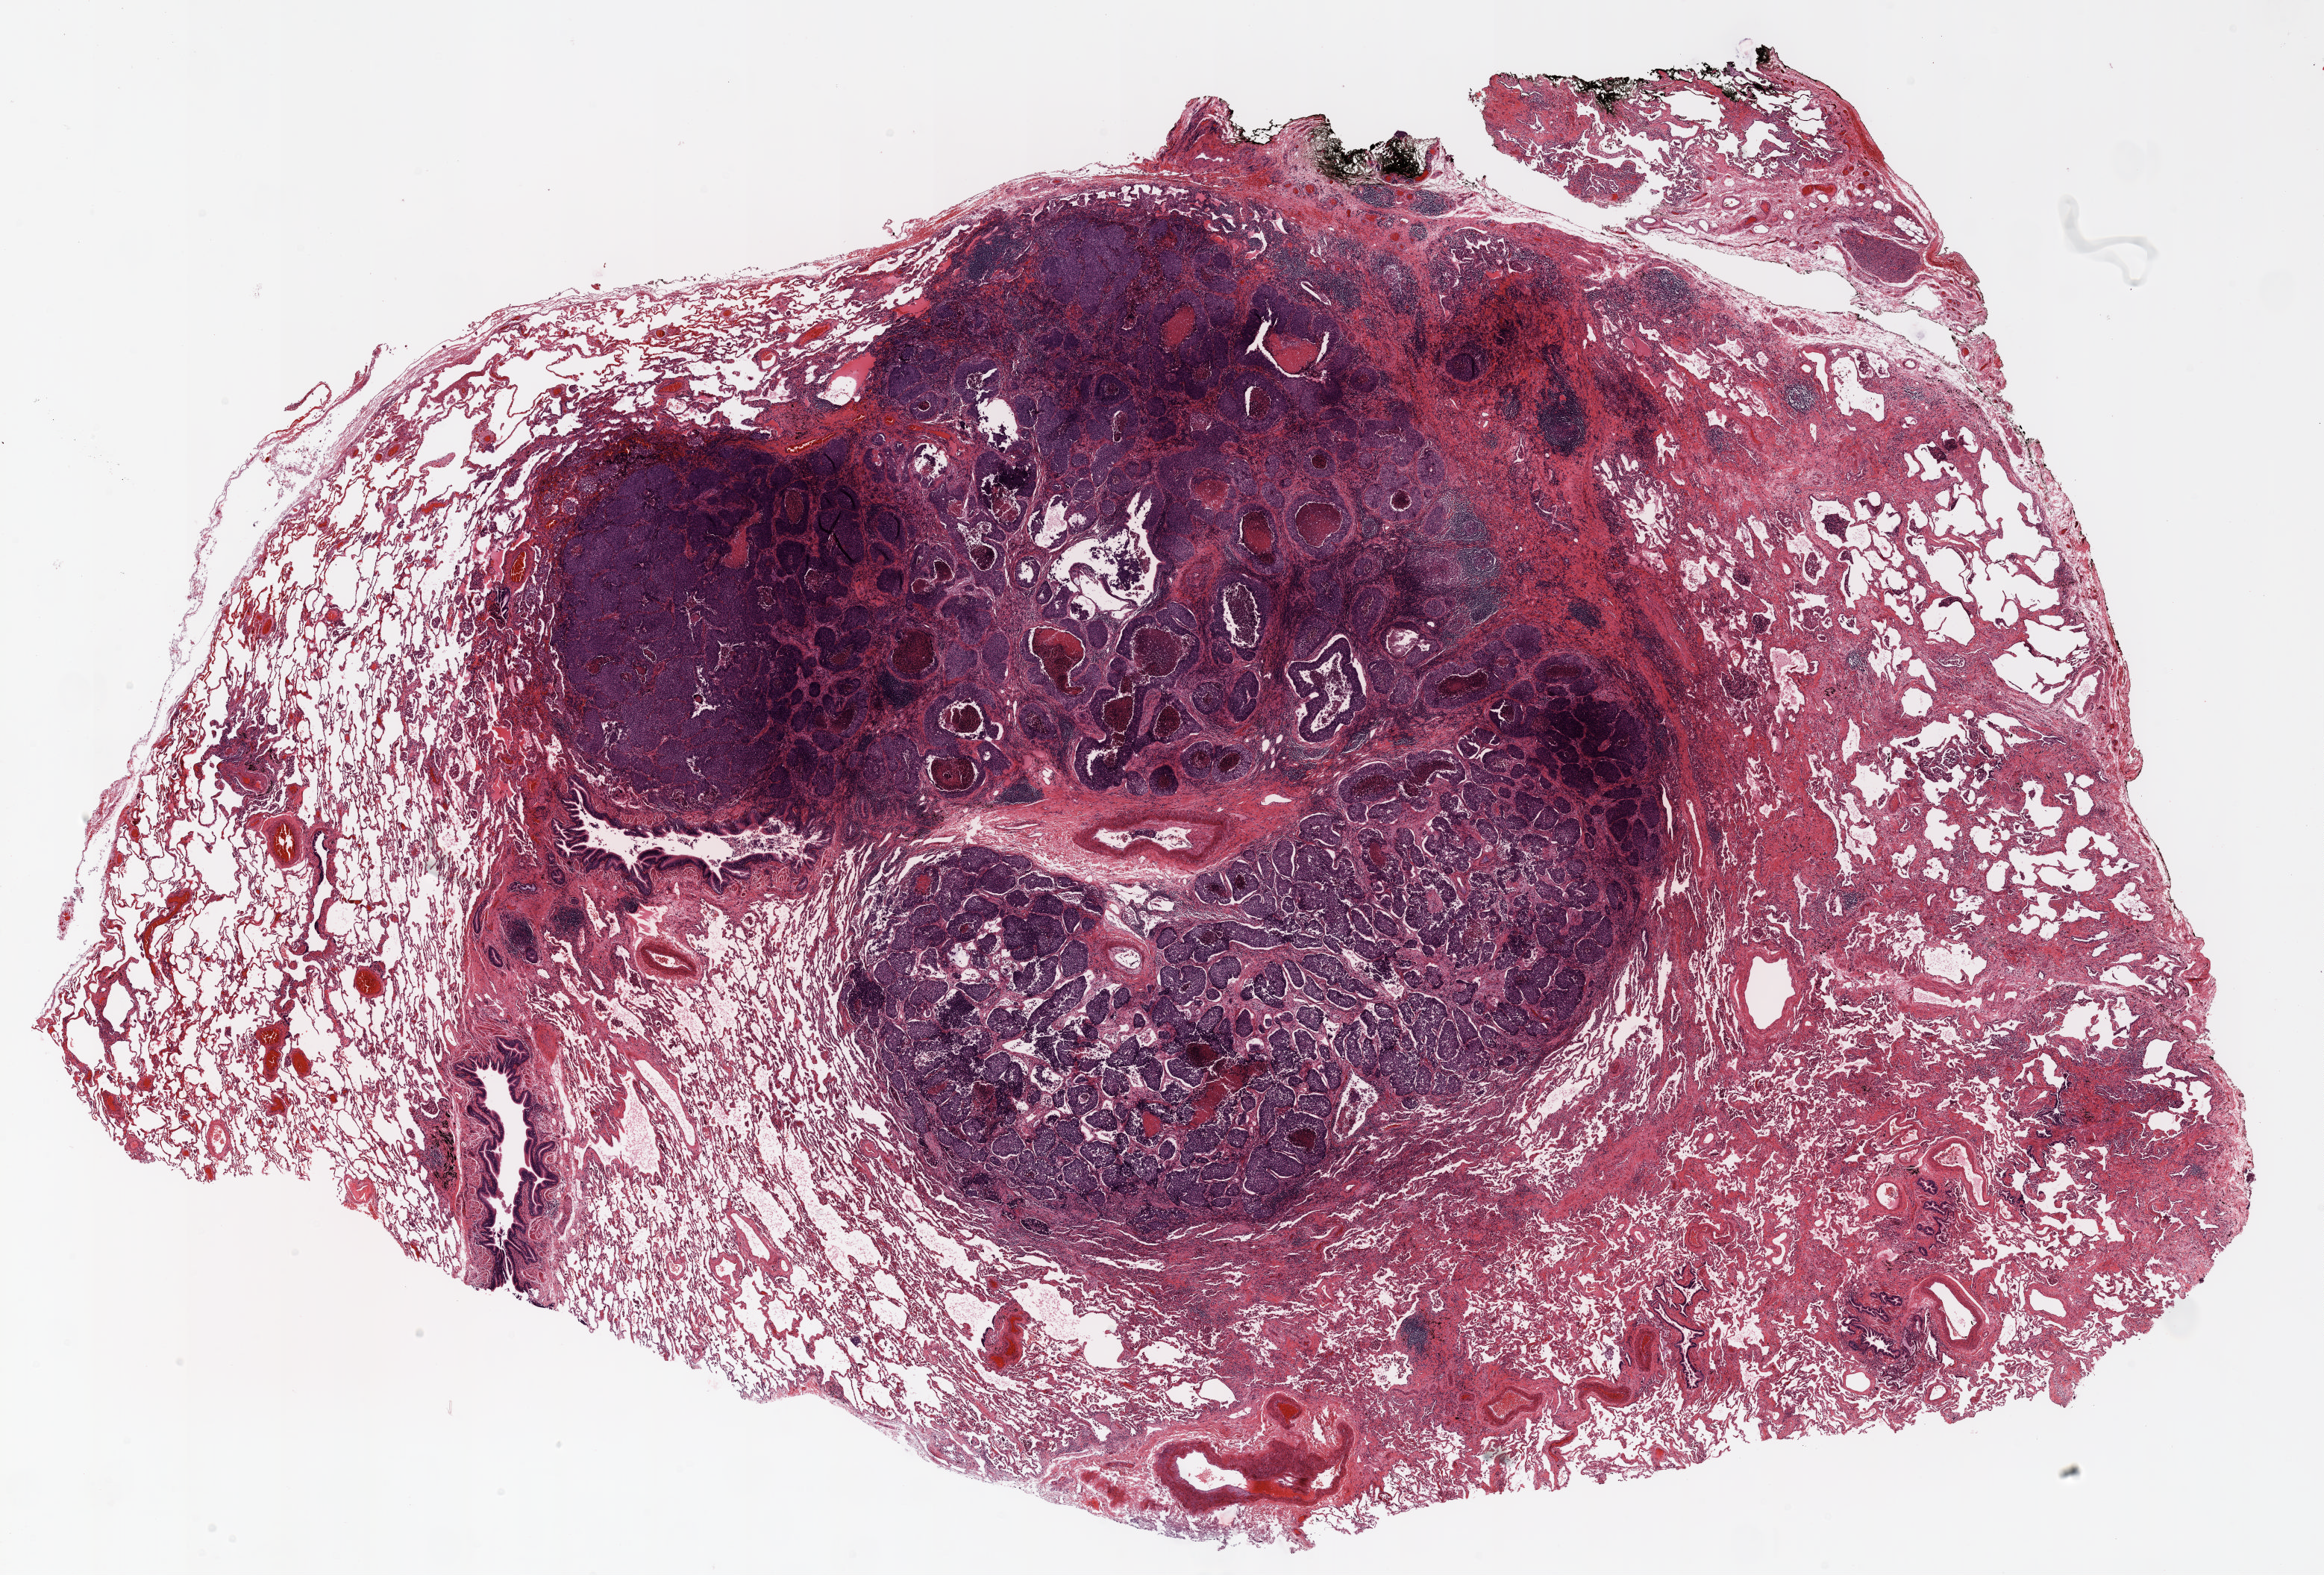
Whole-slide histology image, H&E-stained — whole scanned area (about 25.0 x 17.0 mm, acquisition: 20x scan) shown as a low-resolution overview, FFPE section, lung. Male, age 61 at enrolment. Grade: poorly differentiated (G3).
* tumour size (pathology): 17 mm
* stage (AJCC 6th edition): IA
* ICD-O-3 topography: lower lobe of lung (C34.3)
* participant's lung-cancer diagnosis: Adenocarcinoma, NOS (ICD-O-3 8140/3)
* primary tumour location (clinical record): left lower lobe